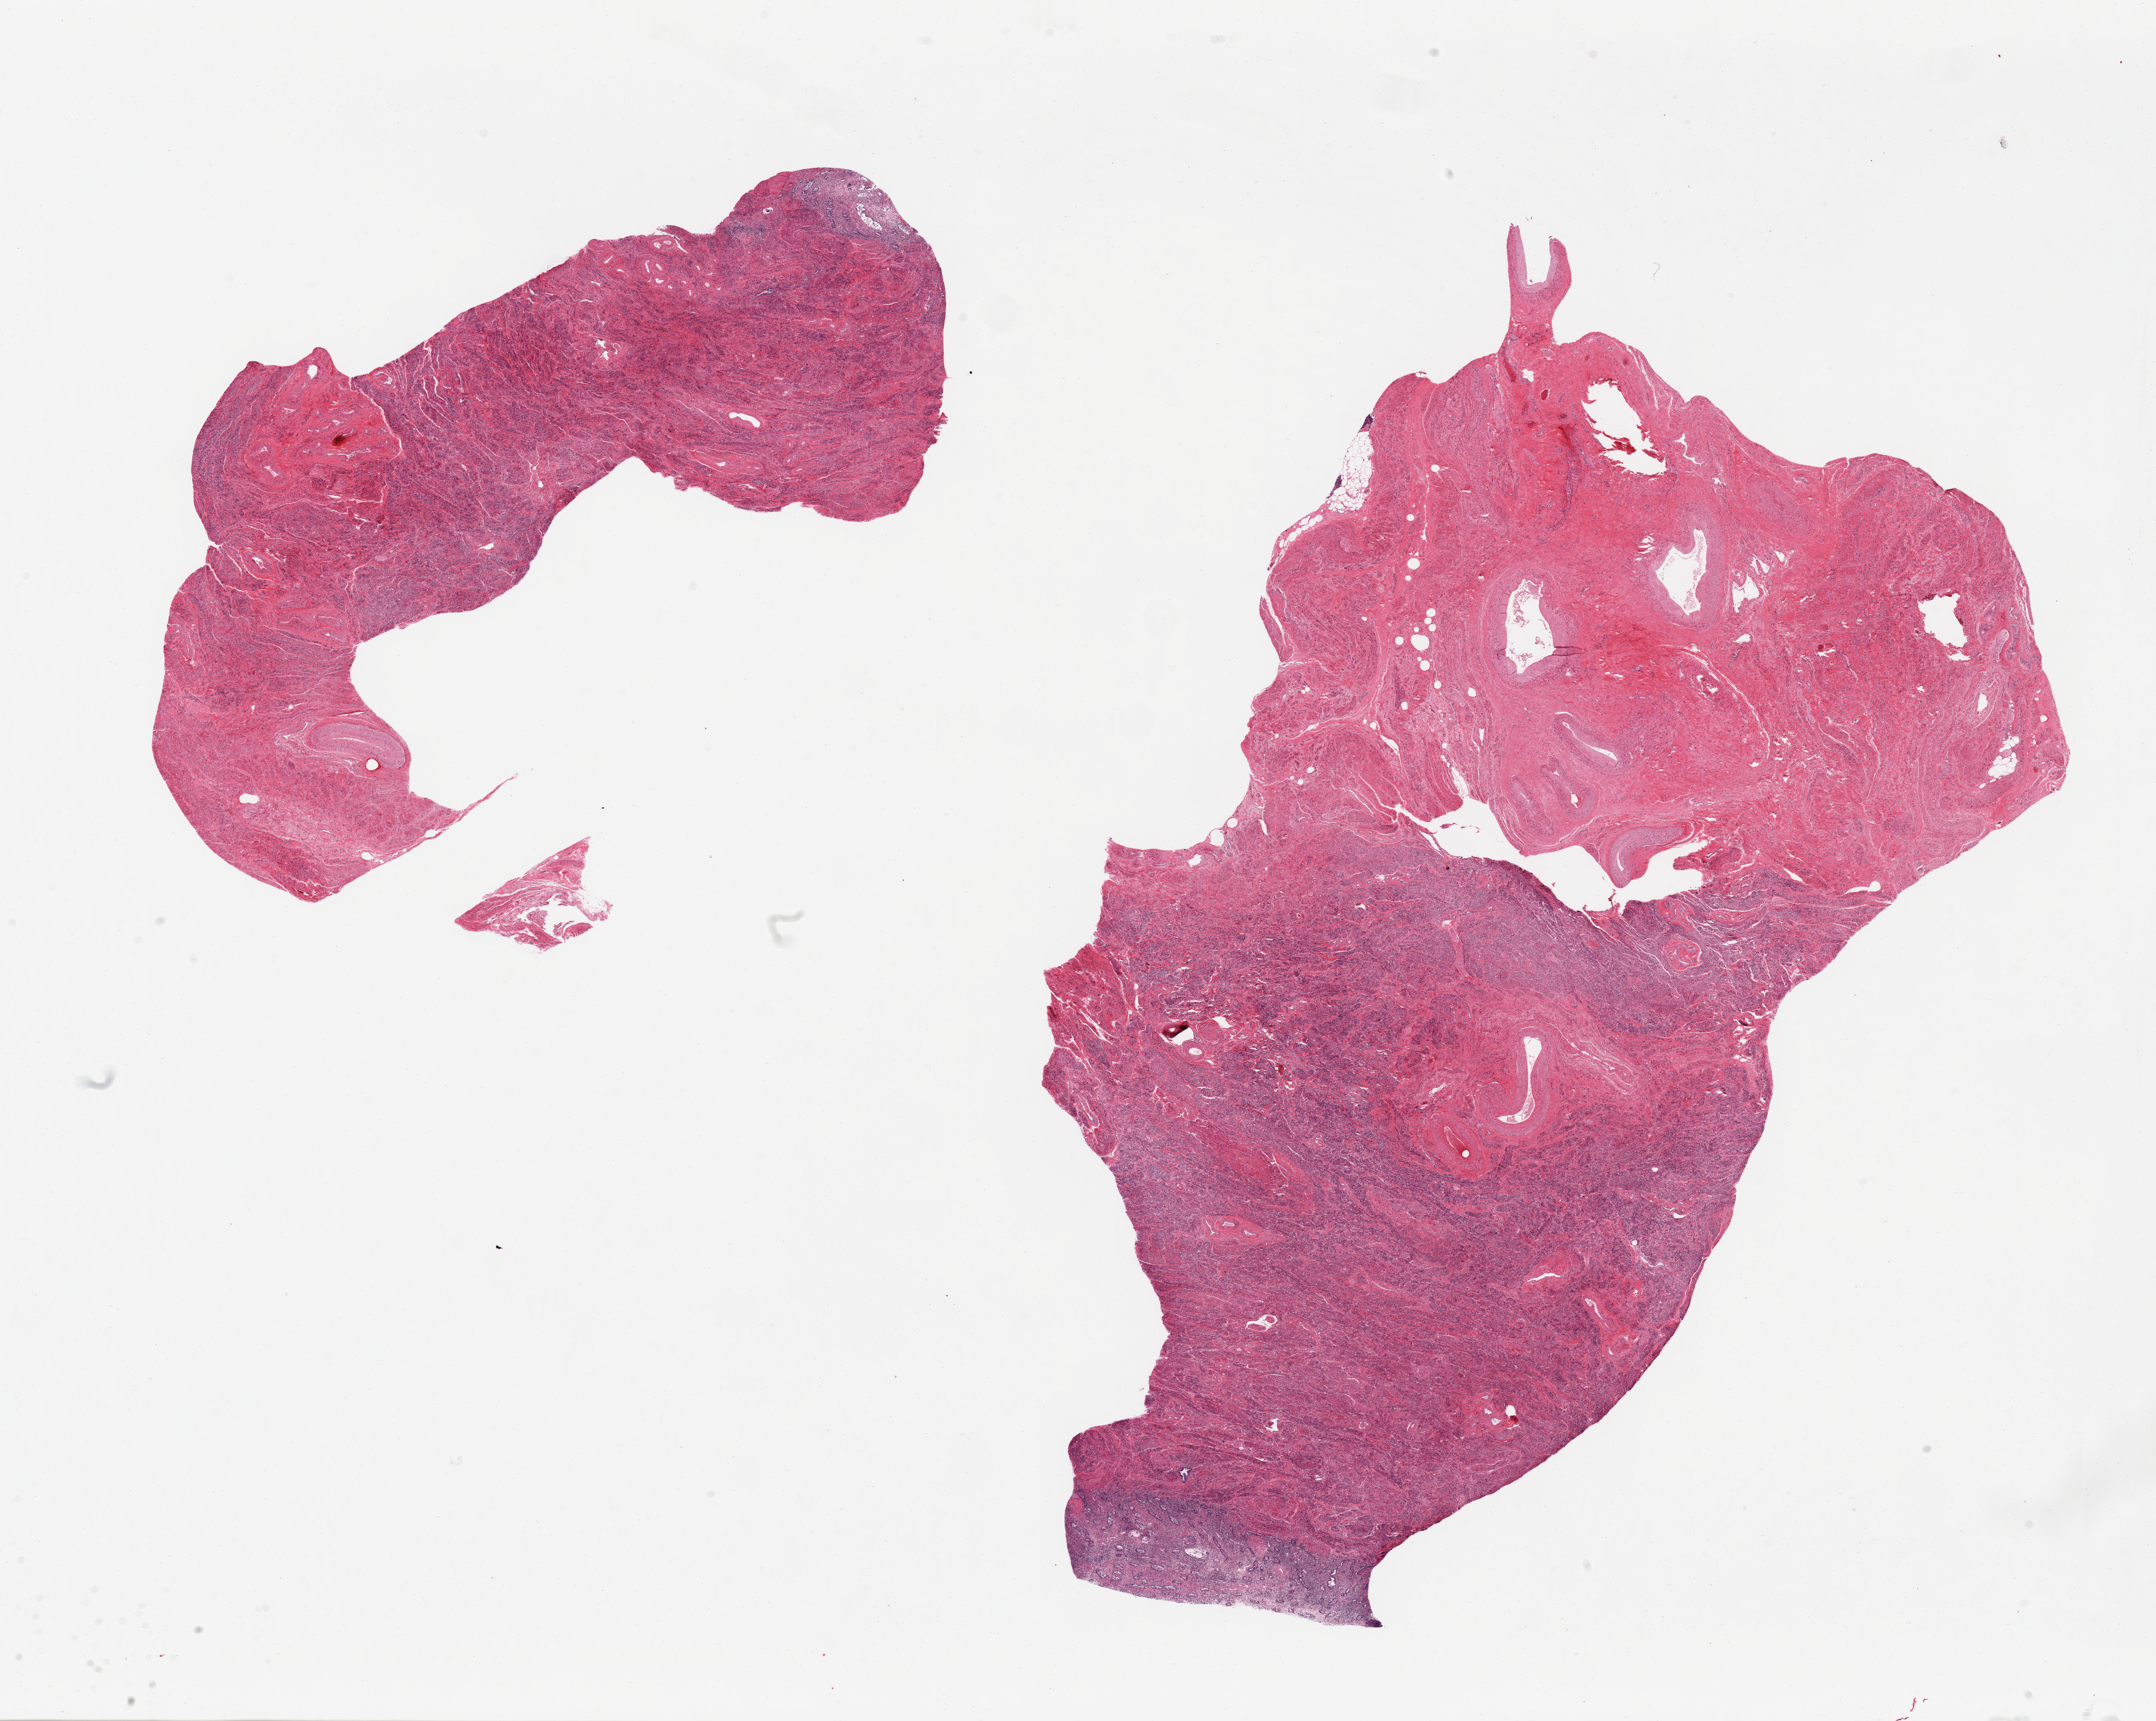
H&E whole-slide image — whole scanned area (about 28.5 x 22.8 mm) shown as a low-resolution overview, PAXgene-fixed, paraffin-embedded tissue, section of uterus (target tissue), tissue donor sample.
Pathologist's review note for this sample: 2 pieces, includes both endometrium and myometrium.